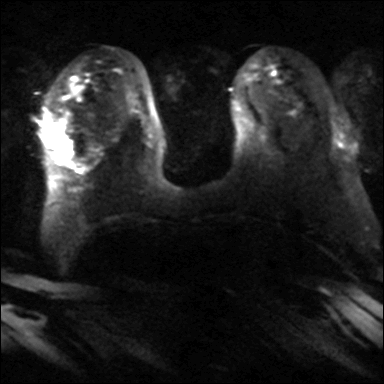
Breast MRI, one axial slice. Position 13 of 40 along the scan axis. Diffusion-weighted series; image 2 of 4 stored at this slice position (different b-values; order by instance number). 3 T. 4 mm slice thickness. 384 × 384 image matrix, field of view 320 × 320 mm. Female patient.
Annotated regions visible in this slice (outlined manually by an expert reader):
- tumour on diffusion-weighted imaging: bounding box <52,126,67,152> (left, top, right, bottom; pixels)